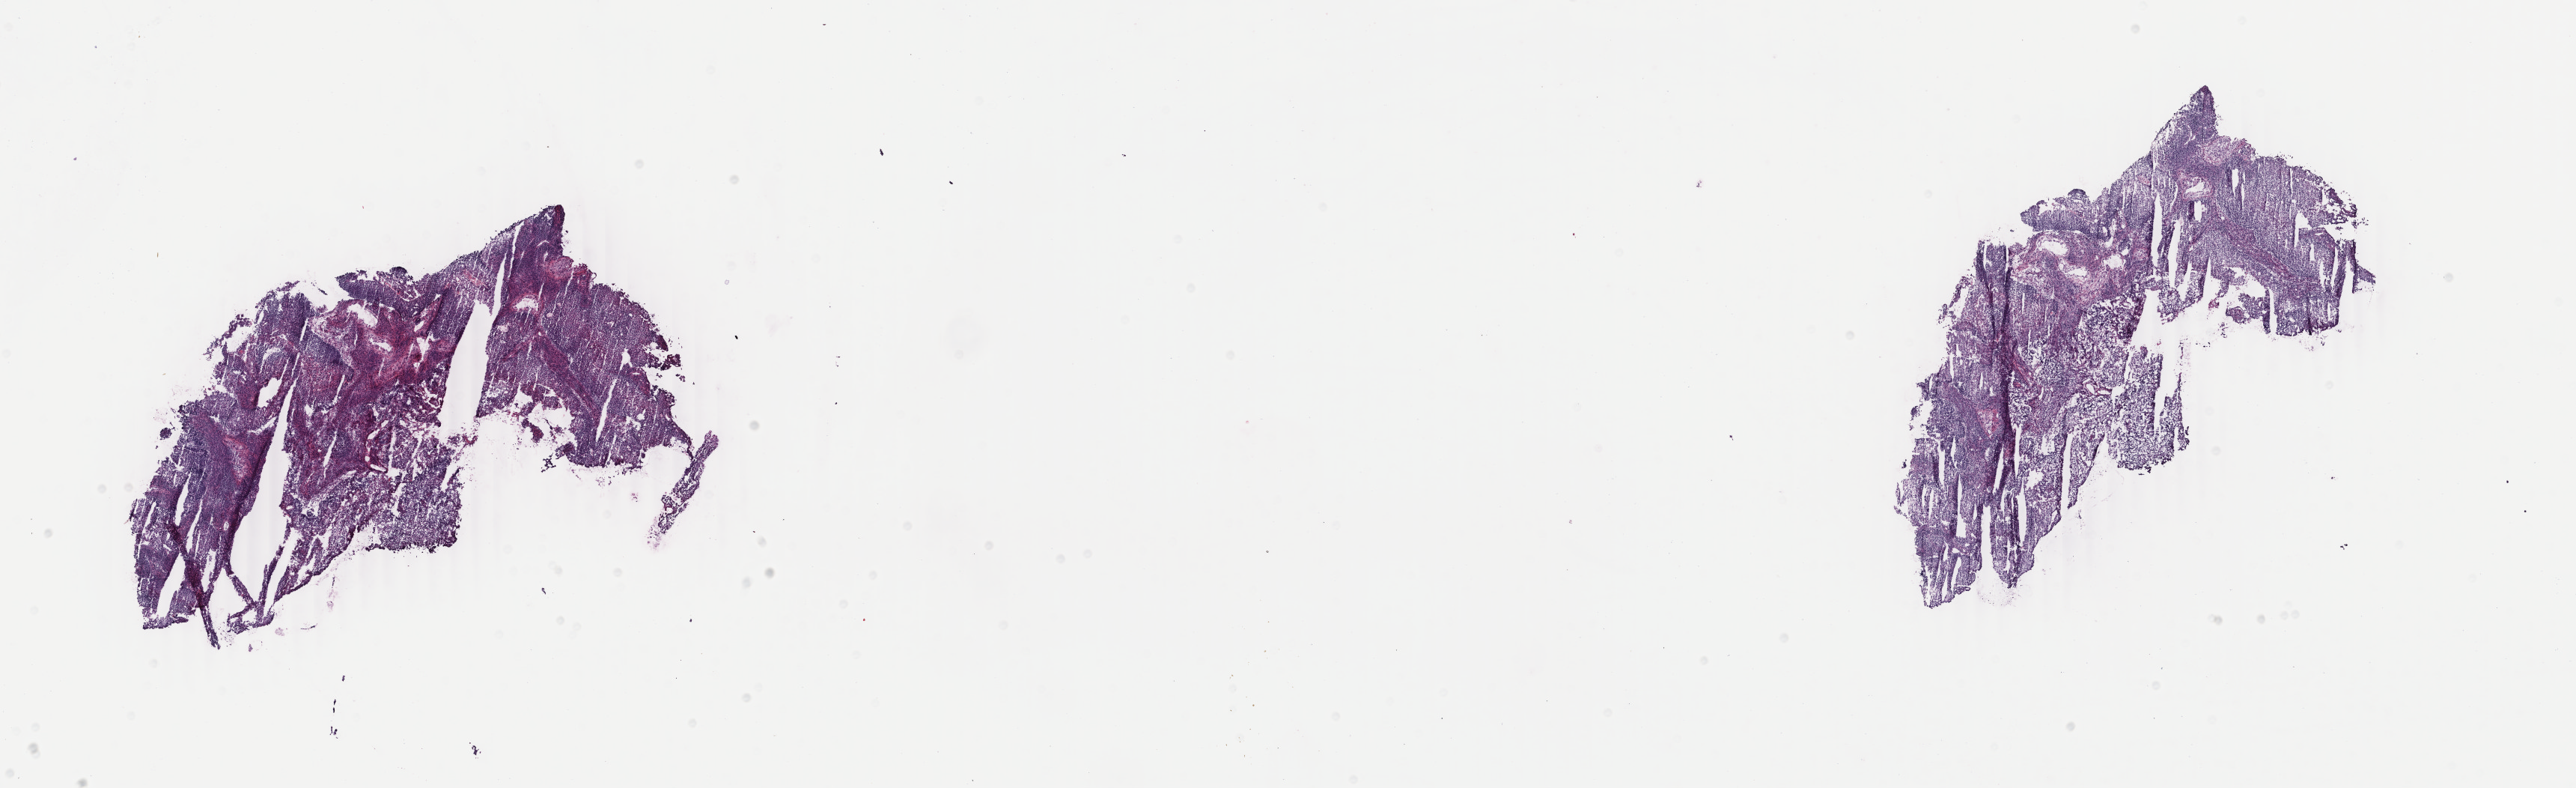
Hematoxylin and eosin (H&E) stained whole-slide image — low-resolution overview of the scanned area, about 27.4 x 8.4 mm (acquisition: 40x scan). Frozen section from the top of the tissue portion. Uterus, primary tumour sample. Patient: female, age at initial diagnosis 59 years. Histologic grade: G3 (poorly differentiated). Pathologist review of this section (percent, as recorded): tumour cells 96%, tumour nuclei 96%, normal cells 0%, stromal cells 2%, necrosis 2%. Infiltration values recorded for this section: lymphocyte infiltration 1%, monocyte infiltration 0%, neutrophil infiltration 0%.
* FIGO stage: IC
* diagnosis: Endometrioid adenocarcinoma, NOS (endometrium)